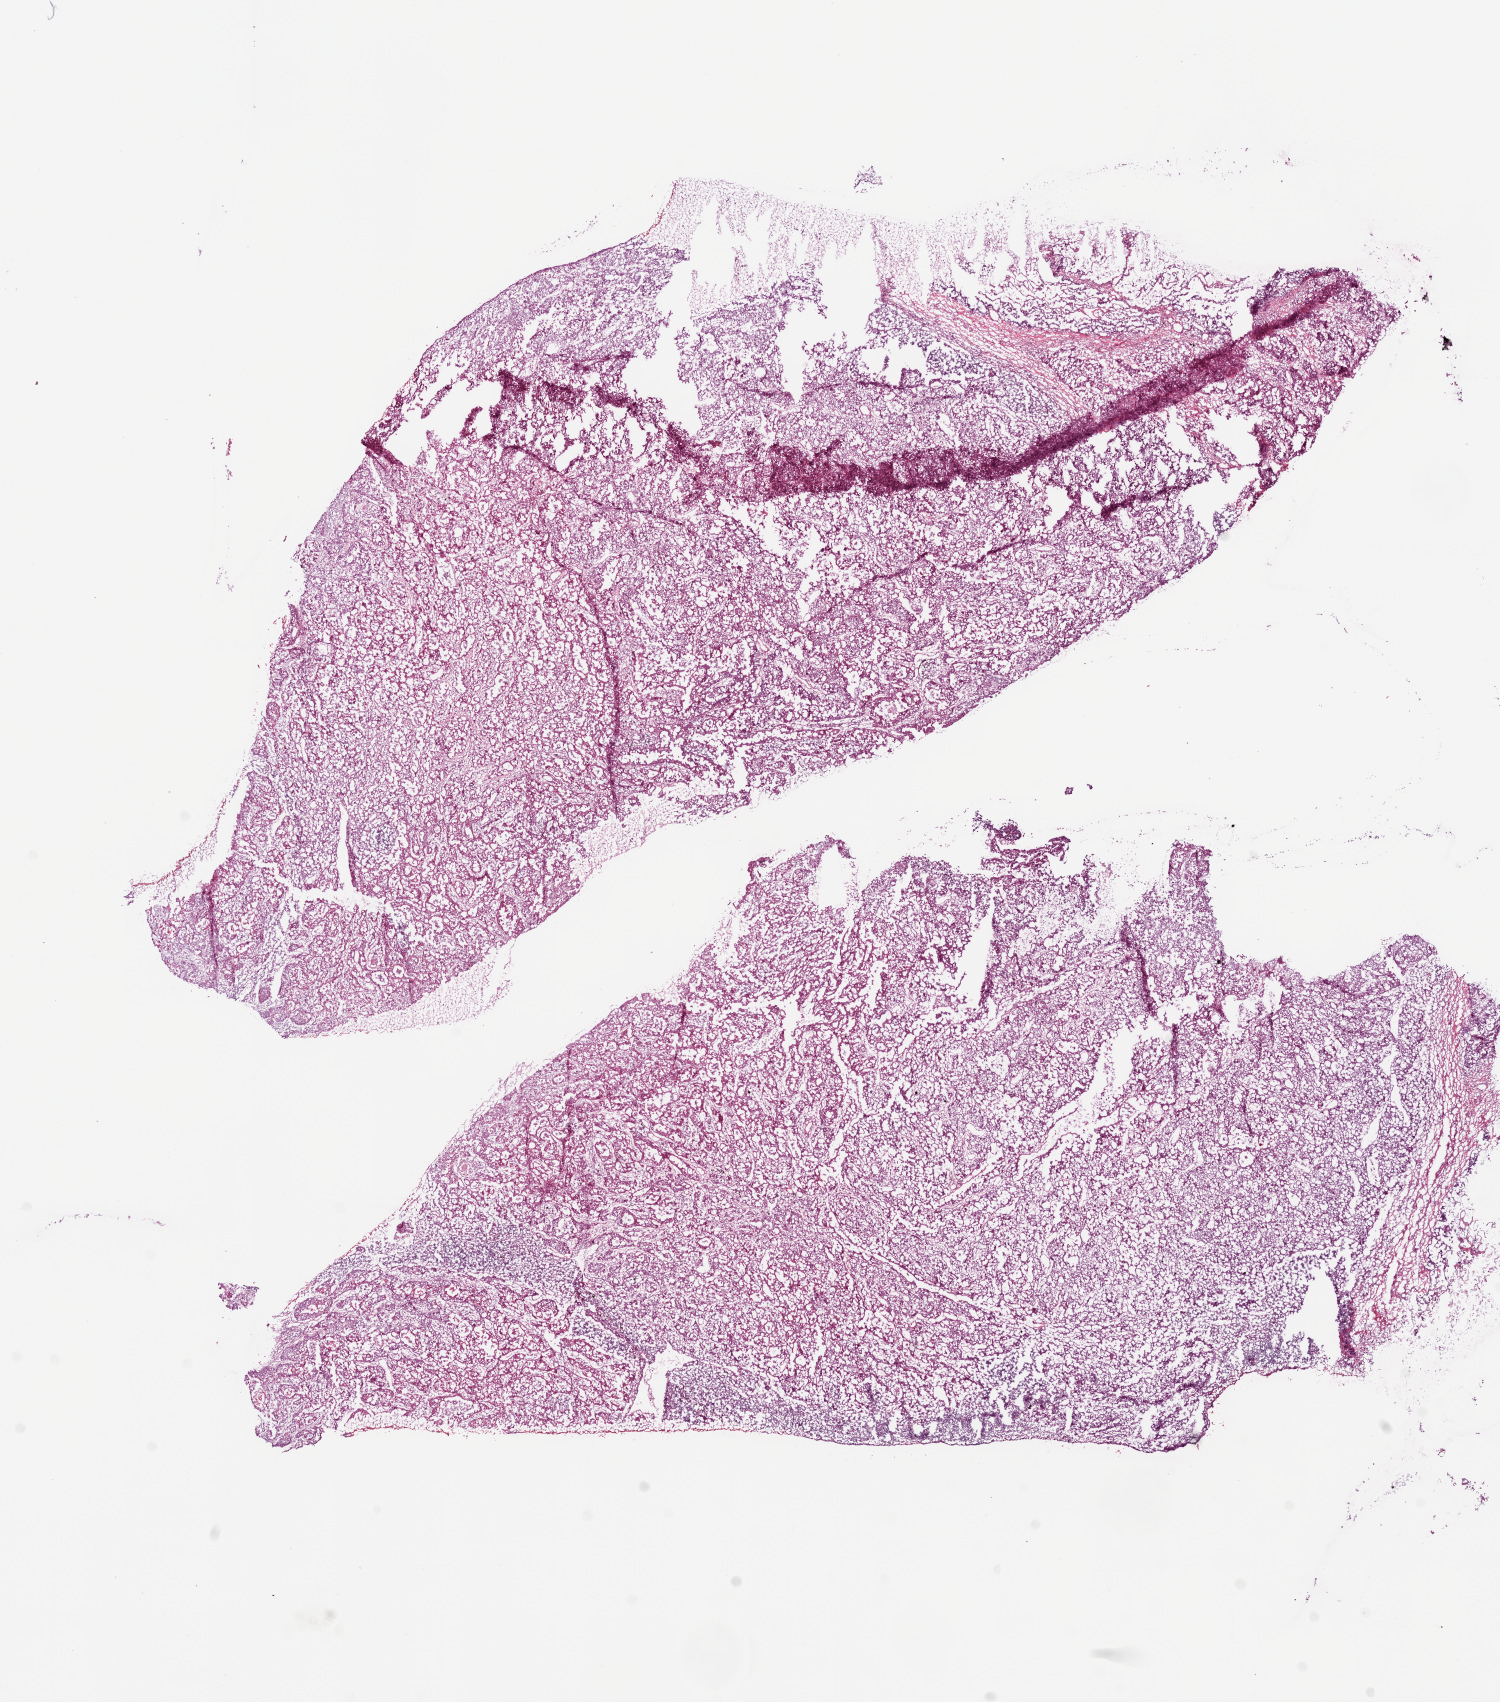
H&E whole-slide image — shown as a low-resolution overview of the whole scanned area (about 12.0 x 13.7 mm, from a 20x scan), frozen section, sample: primary tumour, lung. Patient: male, age at initial diagnosis 44 years. Pathologist review of this section (percent, as recorded): tumour cells 100%, tumour nuclei 80%, normal cells 0%, stromal cells 0%, necrosis 0%. Infiltration values recorded for this section: lymphocyte infiltration 10%, monocyte infiltration 2%, neutrophil infiltration 2%.
Laterality: right. AJCC pathologic stage: IIA. Histologic diagnosis: Basaloid squamous cell carcinoma (lower lobe, lung).